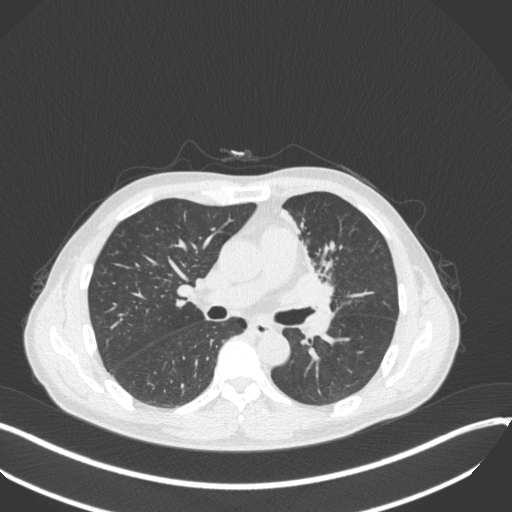
Chest CT, one axial slice. Position 190 of 411 along the scan axis. Reconstruction kernel B31f. 120 kVp. Lung window (W 1500 / L -600 HU). 1 mm slice thickness. 512 × 512 image matrix, field of view 400 × 400 mm. Male patient, age 56 years. Case-level facts recorded for this patient, not image findings: clinical TNM (as recorded): T2a N0 M0.
Outlined on this slice (rectangle marked by the reading radiologist):
- lung tumour (recorded histology: squamous cell carcinoma): bounding box <283,261,341,308> (left, top, right, bottom; pixels)